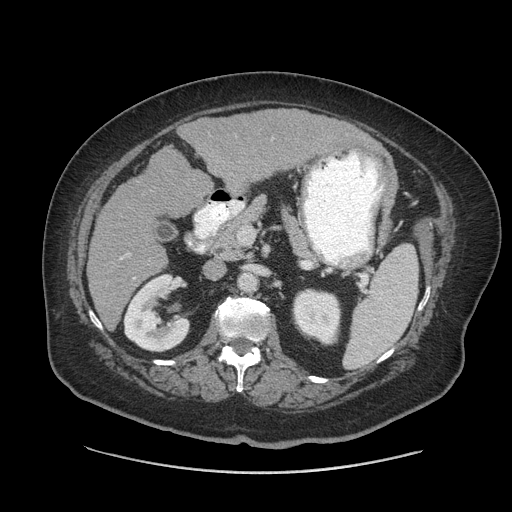
Contrast-enhanced abdominal CT (liver protocol), one axial slice. Position 32 of 91 along the scan axis. 140 kVp. Soft-tissue window (W 400 / L 40 HU). 2.5 mm slice thickness. 512 × 512 image matrix, field of view 420 × 420 mm. From the clinical record (not read from this slice): diagnosis: hepatocellular carcinoma (patient treated with transarterial chemoembolisation; whether this scan precedes or follows treatment is not stated here); TNM stage (as recorded): Stage-I; Child-Pugh class: A; tumour differentiation: well differentiated; tumour nodularity: uninodular.
Outlined on this slice (semi-automatically segmented with operator editing):
- liver parenchyma outside the tumour (the mass and vessels are separate outlines, so this box may not span the whole liver): box from (x=86, y=108) to (x=378, y=329) px